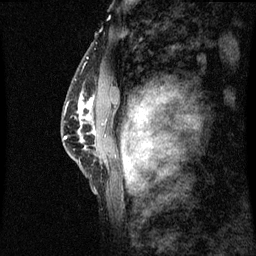
Breast MRI (dynamic contrast-enhanced), one sagittal slice; slice 44 of 60 in the series (ordered by position); dynamic contrast-enhanced series, image 2 of 3 at this slice position (ordered by acquisition); 1.5 T; TE 4.2 ms, TR 8.9 ms; 2 mm slice thickness; 256 × 256 image matrix, field of view 200 × 200 mm. Patient: female, 50 years. From the clinical record (not read from this slice): setting: breast cancer imaged before/during neoadjuvant chemotherapy; receptor status: triple-negative.
Annotated regions visible in this slice (semi-automatically segmented with operator editing):
- analysis volume of interest (the breast-tissue region the enhancement analysis was run in; not a lesion): bounding box (x1, y1, x2, y2) in pixels: (68, 82, 98, 169)
- tumour enhancement mask (voxels above the 70 % enhancement threshold inside the analysis volume of interest): (81, 102, 96, 133)